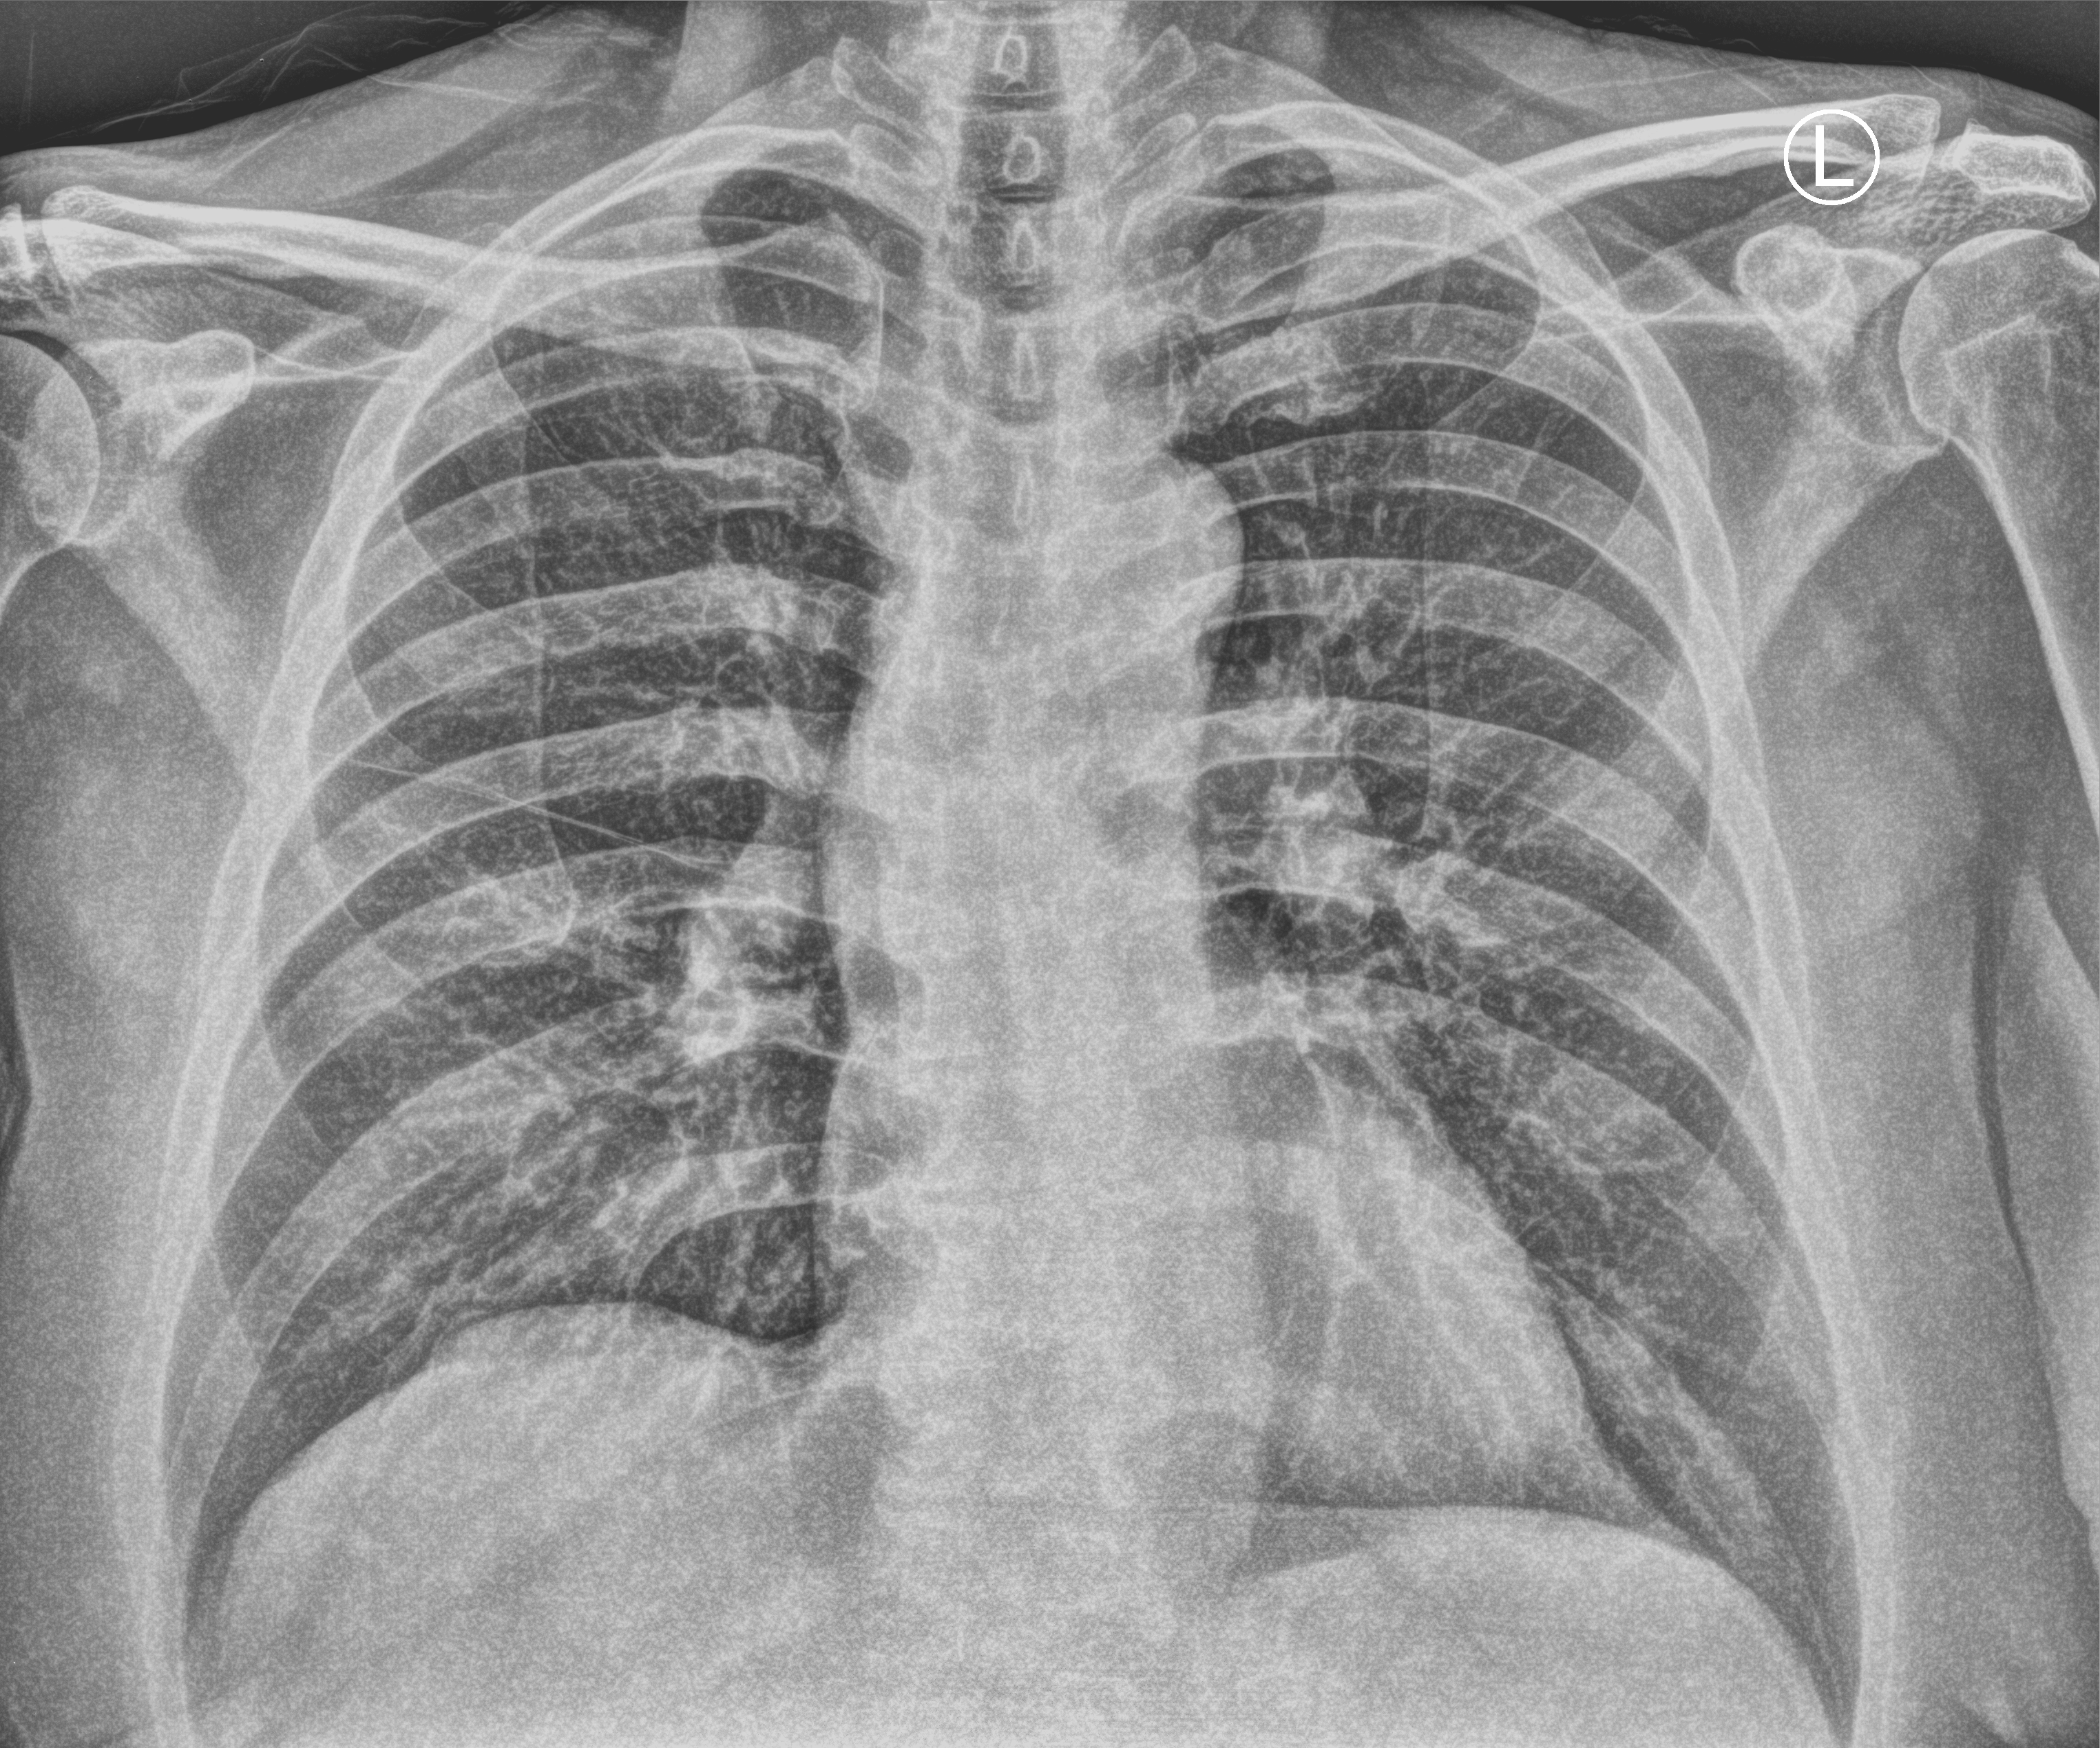
Portable chest radiograph. Patient hospitalised with COVID-19; male, aged 60–74 years.
Hospital-stay facts (about this admission, not read from this image; timing relative to this image not recorded): other chronic lung disease (admission record): no.